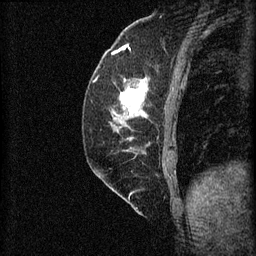
Breast MRI (dynamic contrast-enhanced), one sagittal slice. 3 images stored at this slice position (order not interpretable as contrast timing). 1.5 T. TE 4.2 ms, TR 8.2 ms. 256 × 256 image matrix. Patient: female, 59 years.
Annotated regions visible in this slice (semi-automatic segmentation, software-assisted and operator-edited):
- analysis volume of interest (the breast-tissue region the enhancement analysis was run in; not a lesion): bounding box (x1, y1, x2, y2) in pixels: (92, 74, 152, 131)
- tumour enhancement mask (voxels above the 70 % enhancement threshold inside the analysis volume of interest): (121, 78, 149, 117)